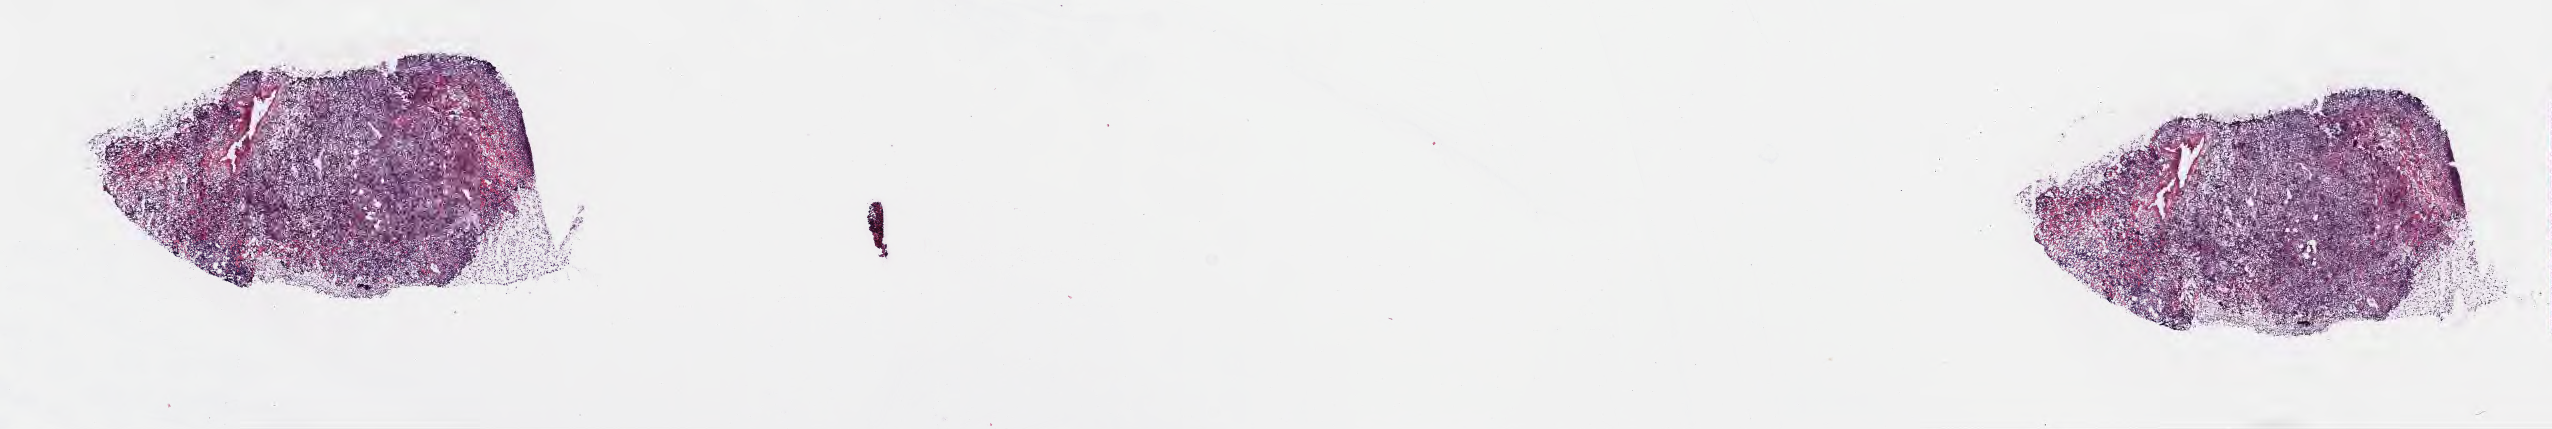
Hematoxylin and eosin (H&E) whole-slide image, shown as a low-resolution overview of the whole scanned area (about 20.6 x 3.5 mm). Cryosection. Primary tumor. Anatomic site: mandible. Patient: male, age at initial diagnosis 7 years. Pathologist review of this section (percent, as recorded): tumor cells 70%, tumor nuclei 80%, stromal cells 20%, necrosis 10%, normal cells 0%. Infiltration values recorded for this section: lymphocyte infiltration 50%, monocyte infiltration 25%, neutrophil infiltration 5%.
Section: bottom of the tissue portion. Diagnosis: Burkitt lymphoma, NOS. Ann Arbor stage (patient): Stage III.